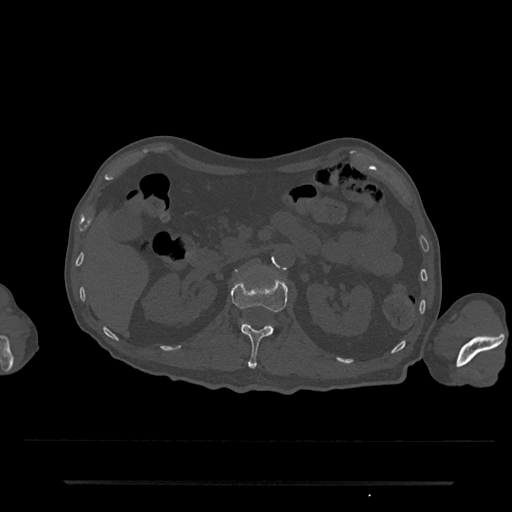
CT including the spine, one axial slice. Slice 114 of 797 in the series (ordered by position). Reconstruction kernel Br40s/3. 120 kVp. Bone window (W 1800 / L 400 HU). 0.5 mm slice thickness. 512 × 512 image matrix. Male patient, age 74 years. Case-level facts recorded for this patient, not image findings: primary cancer: prostate.
Outlined on this slice (semi-automatic segmentation, software-assisted and operator-edited):
- L1 vertebra: bounding box [x1, y1, x2, y2] px = [231, 271, 288, 369]